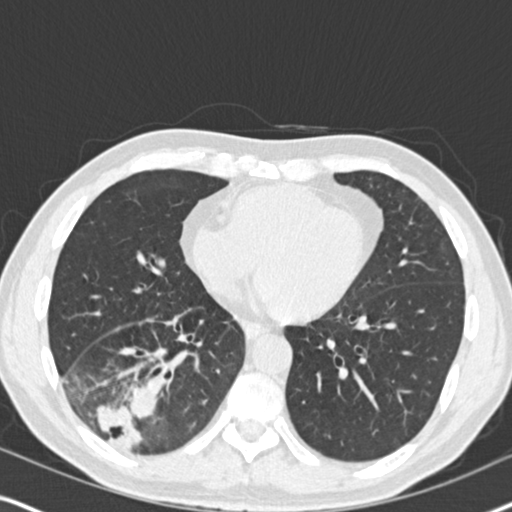
Chest CT (low-dose screening protocol), one axial image. Second annual screen. Lung window (W 1500 / L -600 HU). 2 mm slice thickness. 120 kVp. Slice 105 of 182 in the series. Male, age 61 years at enrolment. Current smoker at enrolment.
Lesion marked by an expert reader, bounding box <54,332,191,465> (left, top, right, bottom; pixels). Reader record for this screening exam (exam-level; its link to the box is not recorded): non-calcified nodule or mass ≥4 mm, right lower lobe, 90 × 80 mm, soft tissue attenuation, pre-existing on the prior screen: yes; interval growth: yes. Participant outcome: lung cancer diagnosed 20 days after this screen — bronchiolo-alveolar adenocarcinoma, NOS, right lower lobe, moderately differentiated (G2), stage IIIB (AJCC 6th edition), 90 mm at pathology.